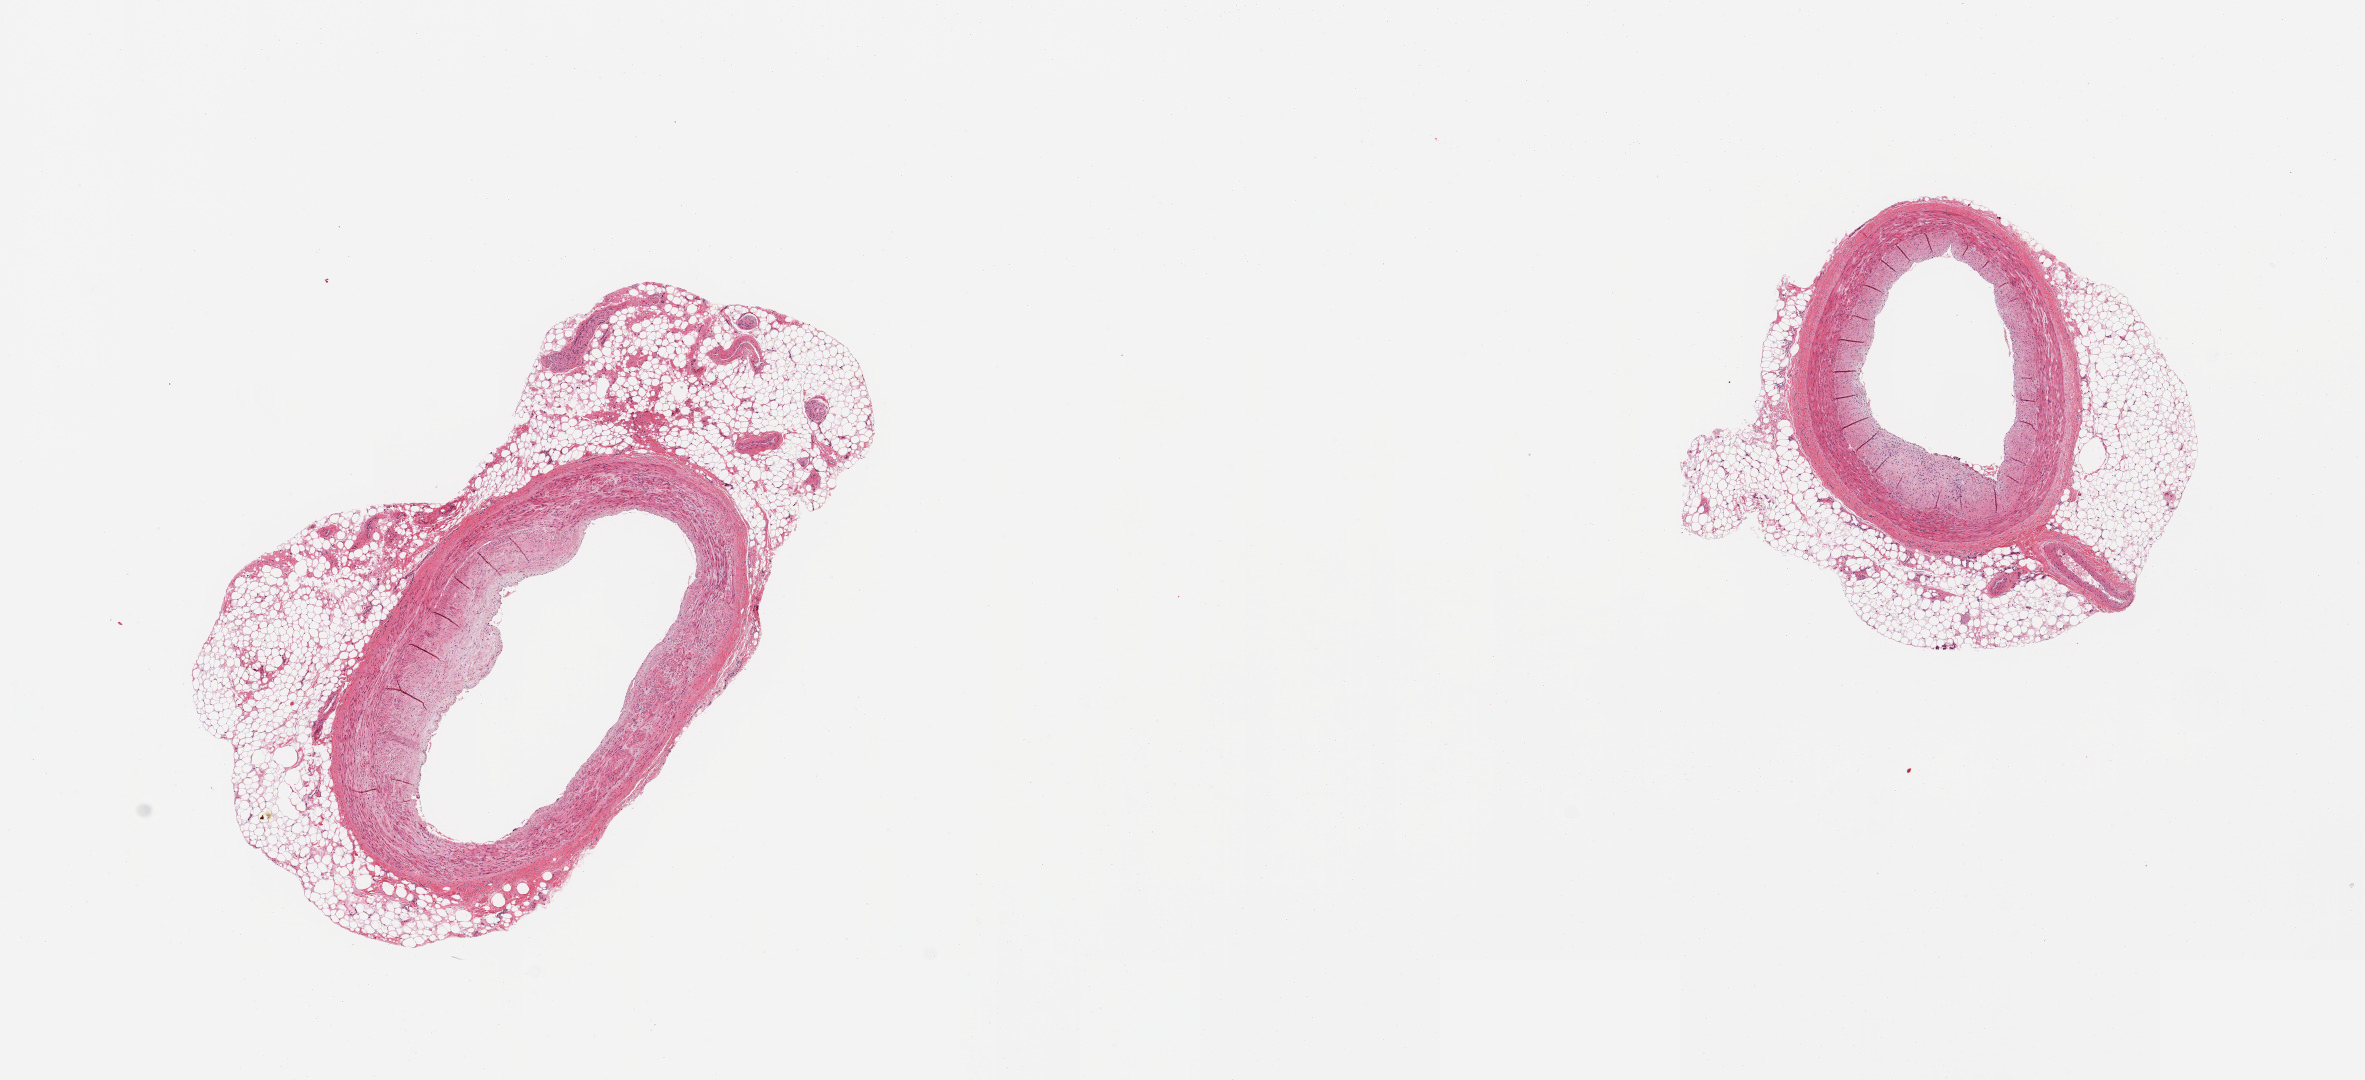
Digitized H&E-stained section — whole scanned area (about 18.7 x 8.5 mm) shown as a low-resolution overview; PAXgene-fixed paraffin-embedded (PFPE) section; target tissue: coronary artery; tissue donor sample. Donor sex: male.
* review note (as recorded): 2 pieces; both include partial rim of fat/nerve (up to 1.5mm, ~50%), plaque